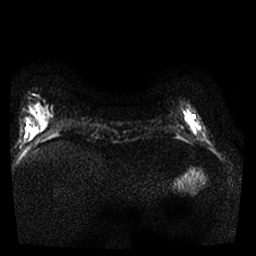
Breast MRI, one axial slice. Position 4 of 25 along the scan axis. Diffusion-weighted series; image 2 of 4 stored at this slice position (different b-values; order by instance number). 1.5 T. 256 × 256 image matrix. Female patient.
Outlined on this slice (expert manual segmentation):
- tumour on diffusion-weighted imaging: bounding box (x1, y1, x2, y2) in pixels: (186, 110, 199, 133)